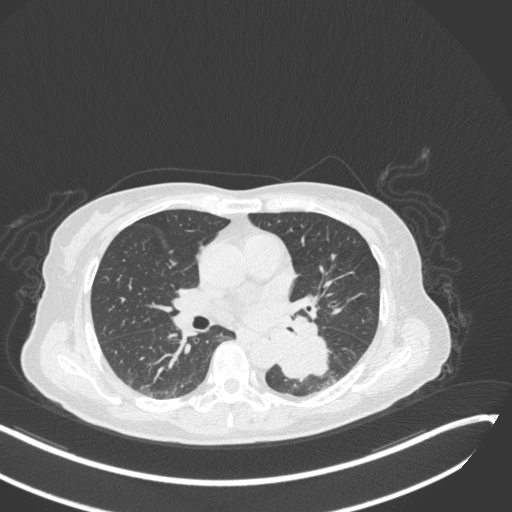
Chest CT, one axial slice. Position 144 of 342 along the scan axis. 120 kVp. Lung window (W 1500 / L -600 HU). 1 mm slice thickness. 512 × 512 image matrix, field of view 400 × 400 mm. Female patient, age 64 years. Case-level facts recorded for this patient, not image findings: clinical TNM (as recorded): T3 N1 M1.
Structures marked on this image (rectangle marked by the reading radiologist):
- lung tumour (recorded histology: small cell carcinoma): box from (x=279, y=328) to (x=340, y=383) px